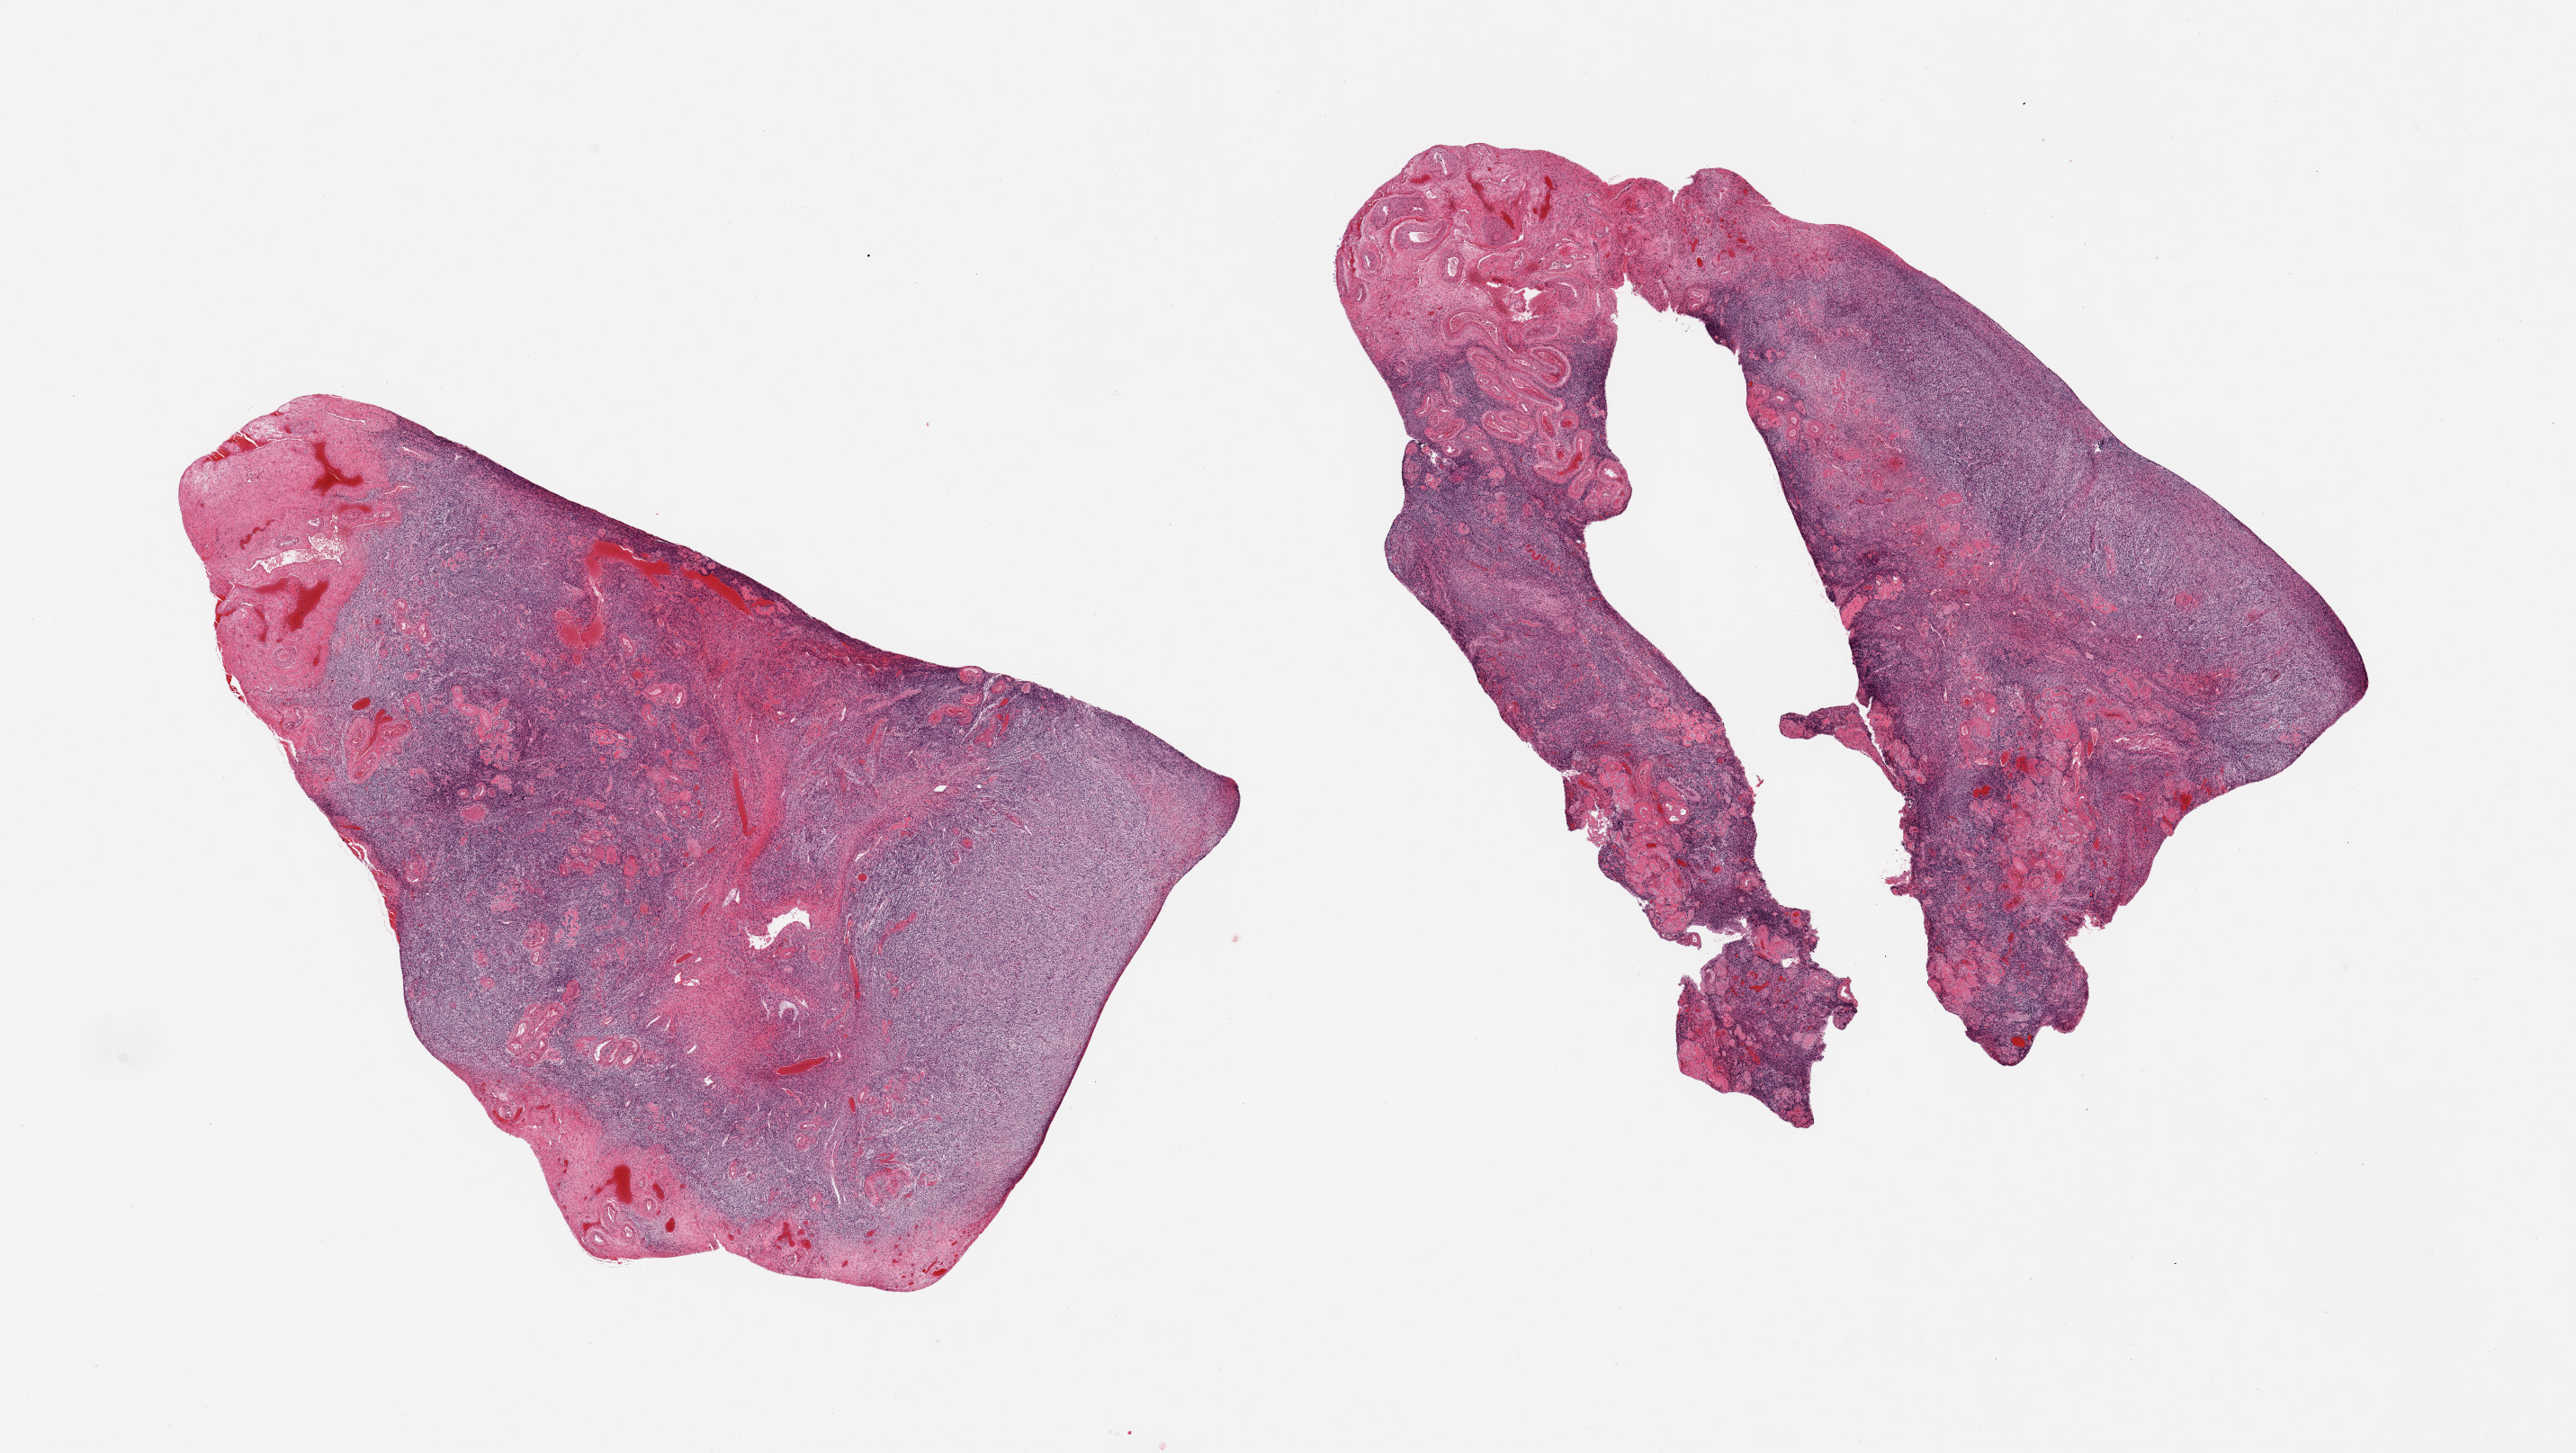
Digitized H&E-stained section, whole scanned area (about 22.6 x 12.8 mm, acquisition: 20x scan) shown as a low-resolution overview, PAXgene-fixed paraffin-embedded (PFPE) section, sampled site (target tissue): ovary, tissue donor sample.
* reviewer comment on this tissue sample: 2 pieces